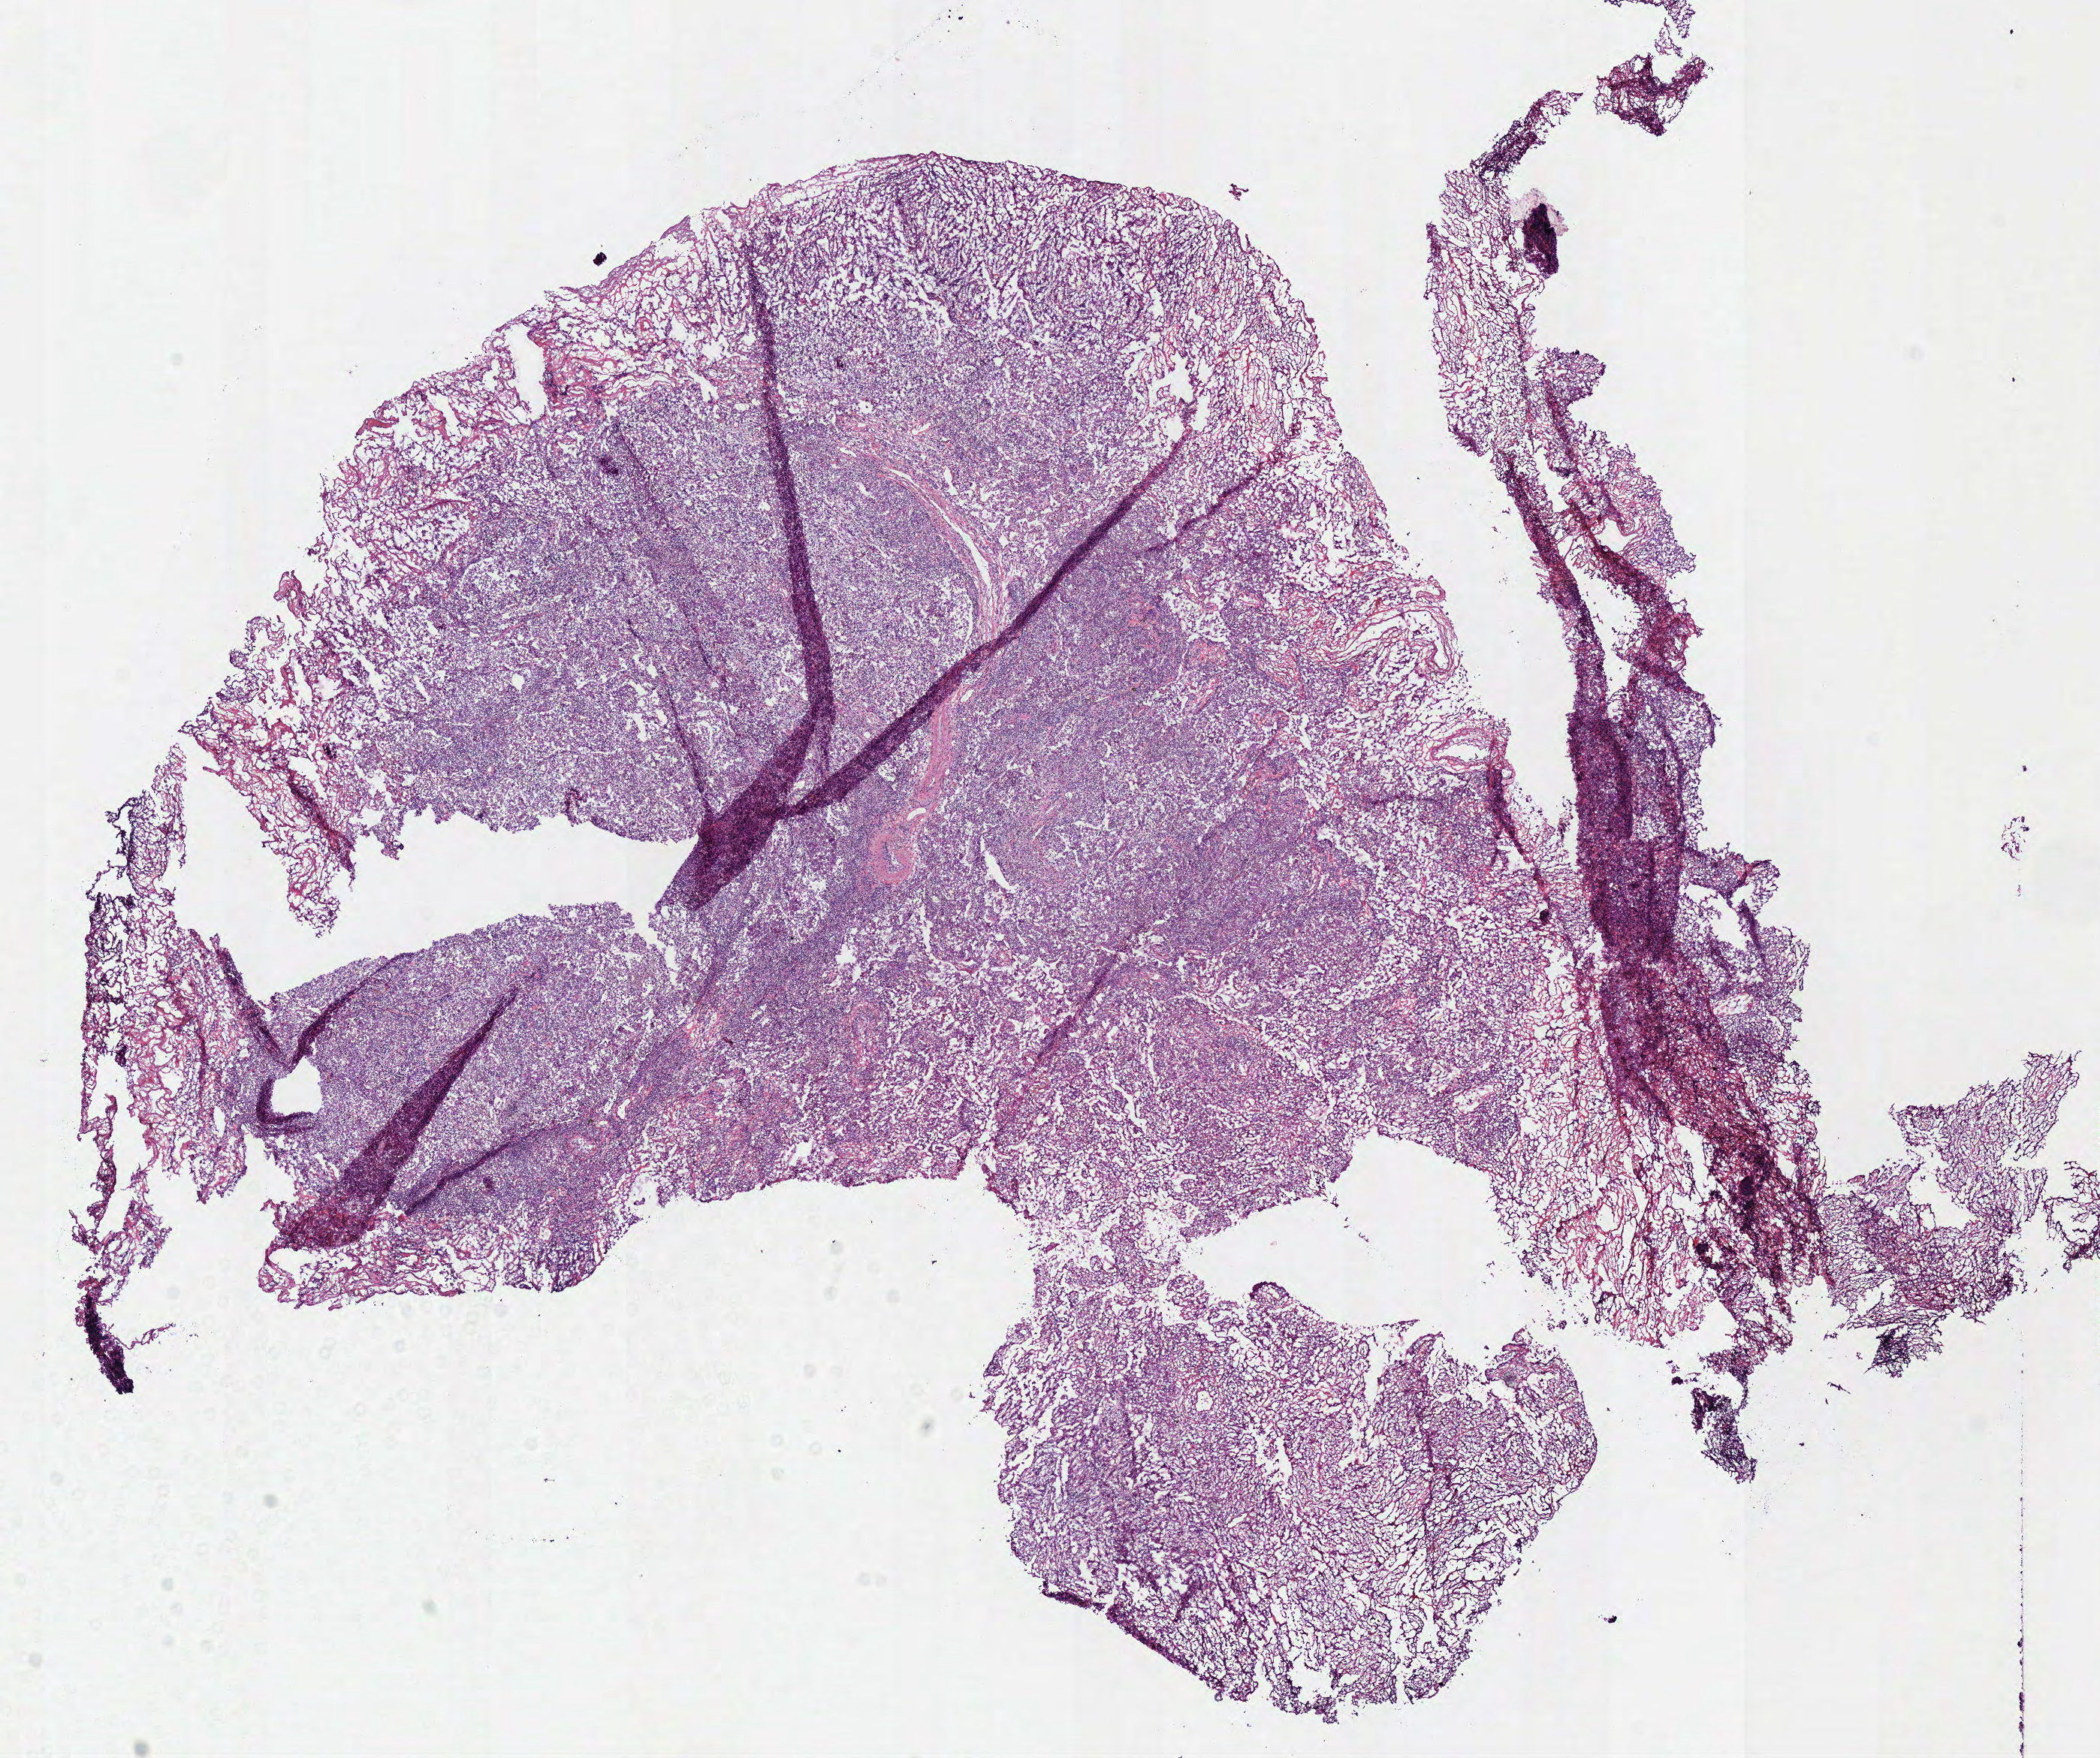
Digitized H&E-stained tissue section (whole slide), low-resolution overview of the scanned area, about 11.0 x 9.2 mm (acquisition: 40x scan); frozen section from the bottom of the tissue portion; sample: primary tumour, lung. Patient: female, age at initial diagnosis 73 years. Pathologist review of this section (percent, as recorded): tumour cells 90%, tumour nuclei 80%, normal cells 0%, stromal cells 10%, necrosis 0%.
Pathologic diagnosis: Adenocarcinoma with mixed subtypes (upper lobe, lung). AJCC pathologic stage: IIA (7th edition).